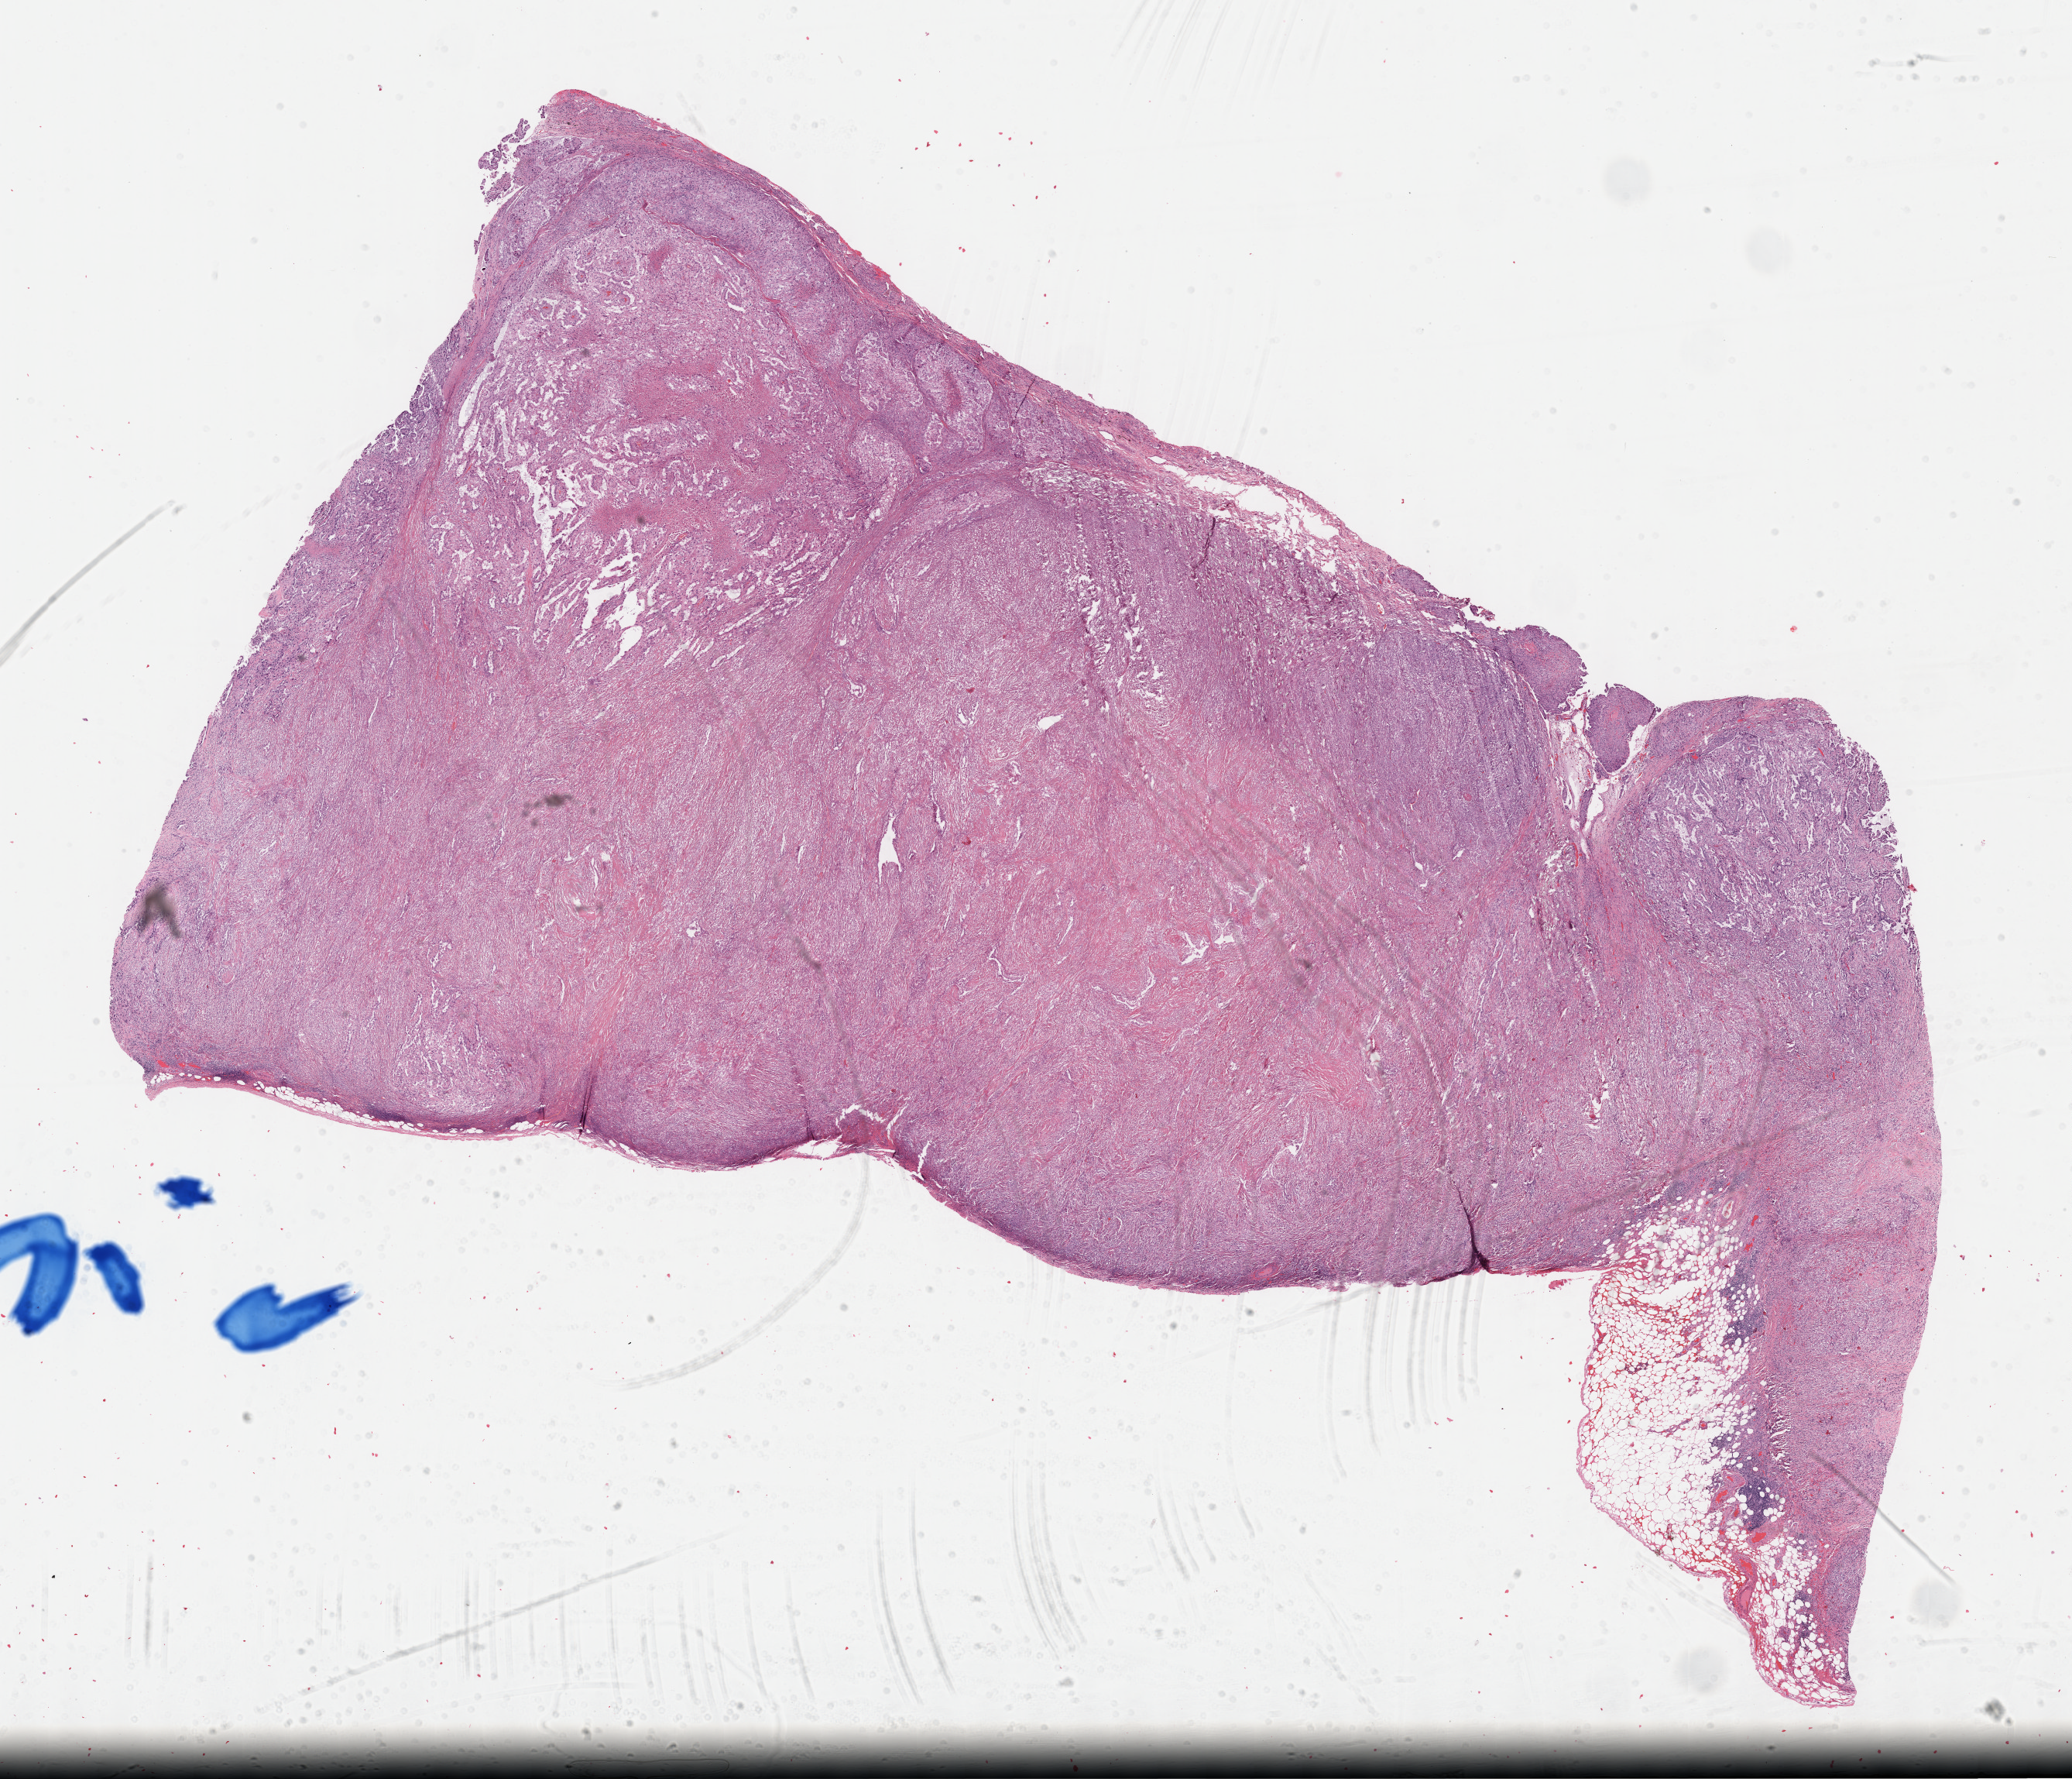
Digitized H&E tissue section (whole slide) — shown as a low-resolution overview of the whole scanned area (about 21.6 x 18.6 mm); formalin-fixed paraffin-embedded (FFPE) diagnostic section; sample: primary tumour, mesothelium. Male patient; age at initial diagnosis 62 years.
* TNM: T3 N3 MX
* AJCC pathologic stage: IV (6th edition)
* diagnosis: Epithelioid mesothelioma, malignant (pleura, NOS)